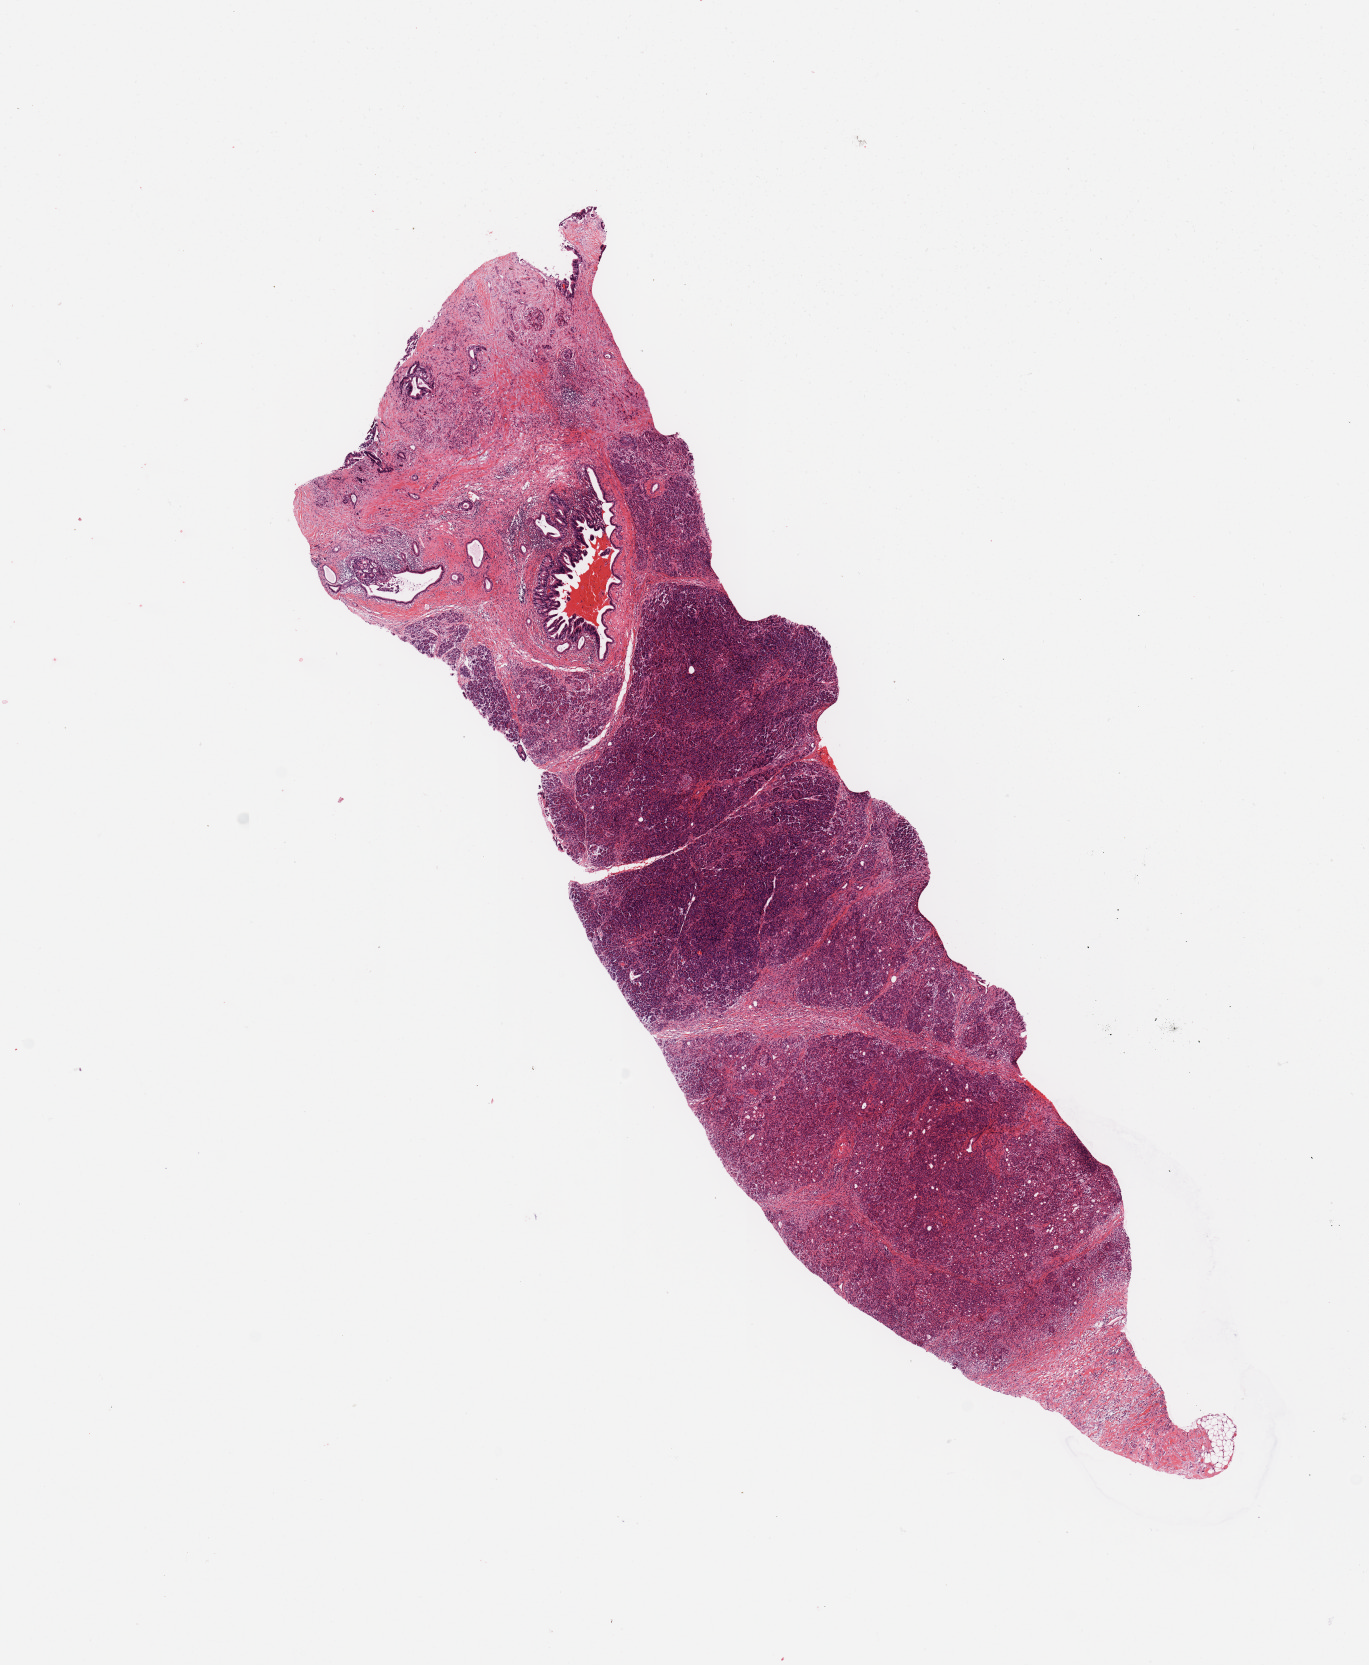
Digitized Hematoxylin and eosin (H&E) stained tissue section (whole slide) — low-resolution overview of the scanned area, about 10.8 x 13.2 mm (slide scanned at 20x), tumour tissue sample, sampled site: pancreas. 63-year-old male patient. Histologic grade: G2 (moderately differentiated). Slide review estimates, as recorded: tumour nuclei 8%, necrosis 0%.
Histologic diagnosis: Infiltrating duct carcinoma, NOS. Primary tumour site (as recorded): tail. AJCC pathologic stage: IB.